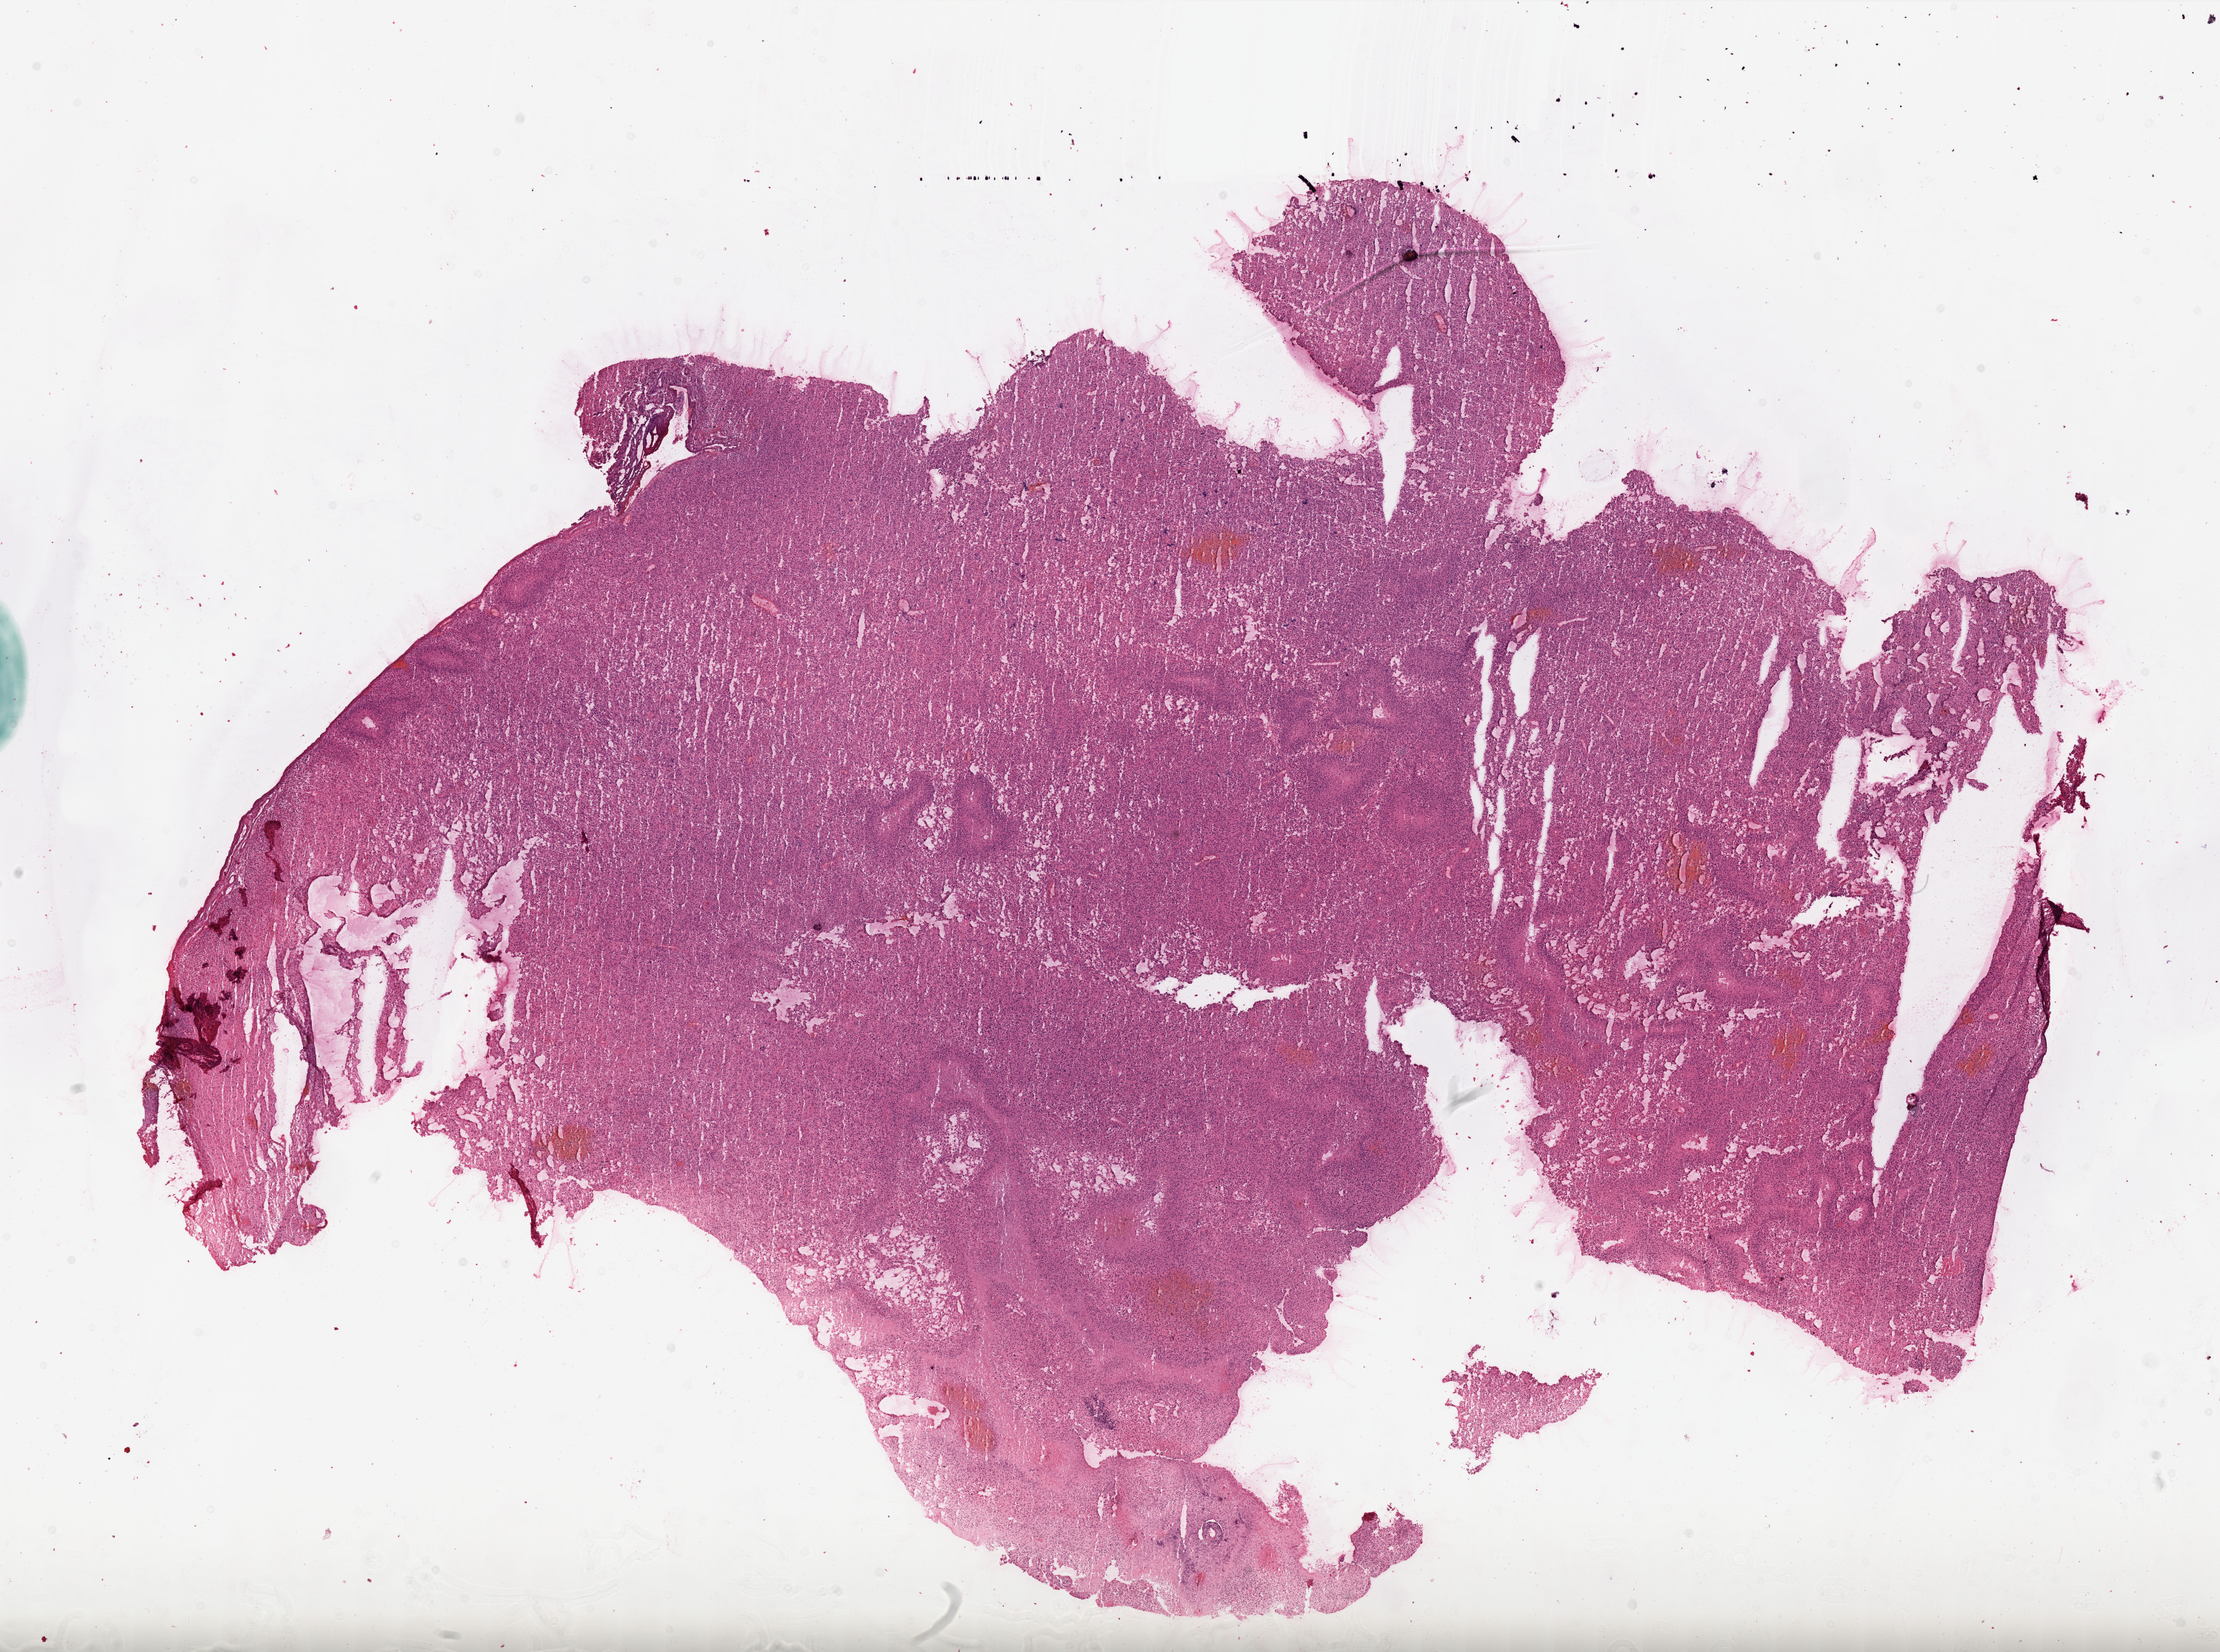
Whole-slide histology image, H&E-stained, whole scanned area (about 24.1 x 17.9 mm, acquisition: 20x scan) shown as a low-resolution overview; frozen section from the top of the tissue portion; brain, primary tumour sample. Female, age 59 years at initial diagnosis. Composition of this section per pathologist review: tumour cells 80%, tumour nuclei 100%, normal cells 0%, stromal cells 0%, necrosis 20%.
Pathologic diagnosis: Glioblastoma.